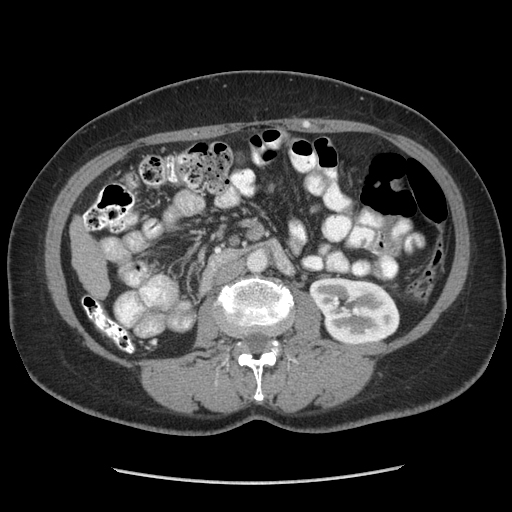
Contrast-enhanced abdominal CT (liver protocol), one axial slice. Position 113 of 185 along the scan axis. Reconstruction kernel STANDARD. 140 kVp. Soft-tissue window (W 400 / L 40 HU). 2.5 mm slice thickness. 512 × 512 image matrix, field of view 360 × 360 mm. From the clinical record (not read from this slice): diagnosis: hepatocellular carcinoma (patient treated with transarterial chemoembolisation; whether this scan precedes or follows treatment is not stated here); TNM stage (as recorded): Stage-I; Child-Pugh class: A; tumour differentiation: poorly differentiated.
Outlined on this slice (semi-automatically segmented with operator editing):
- liver parenchyma outside the tumour (the mass and vessels are separate outlines, so this box may not span the whole liver): bounding box (x1, y1, x2, y2) in pixels: (70, 218, 108, 296)